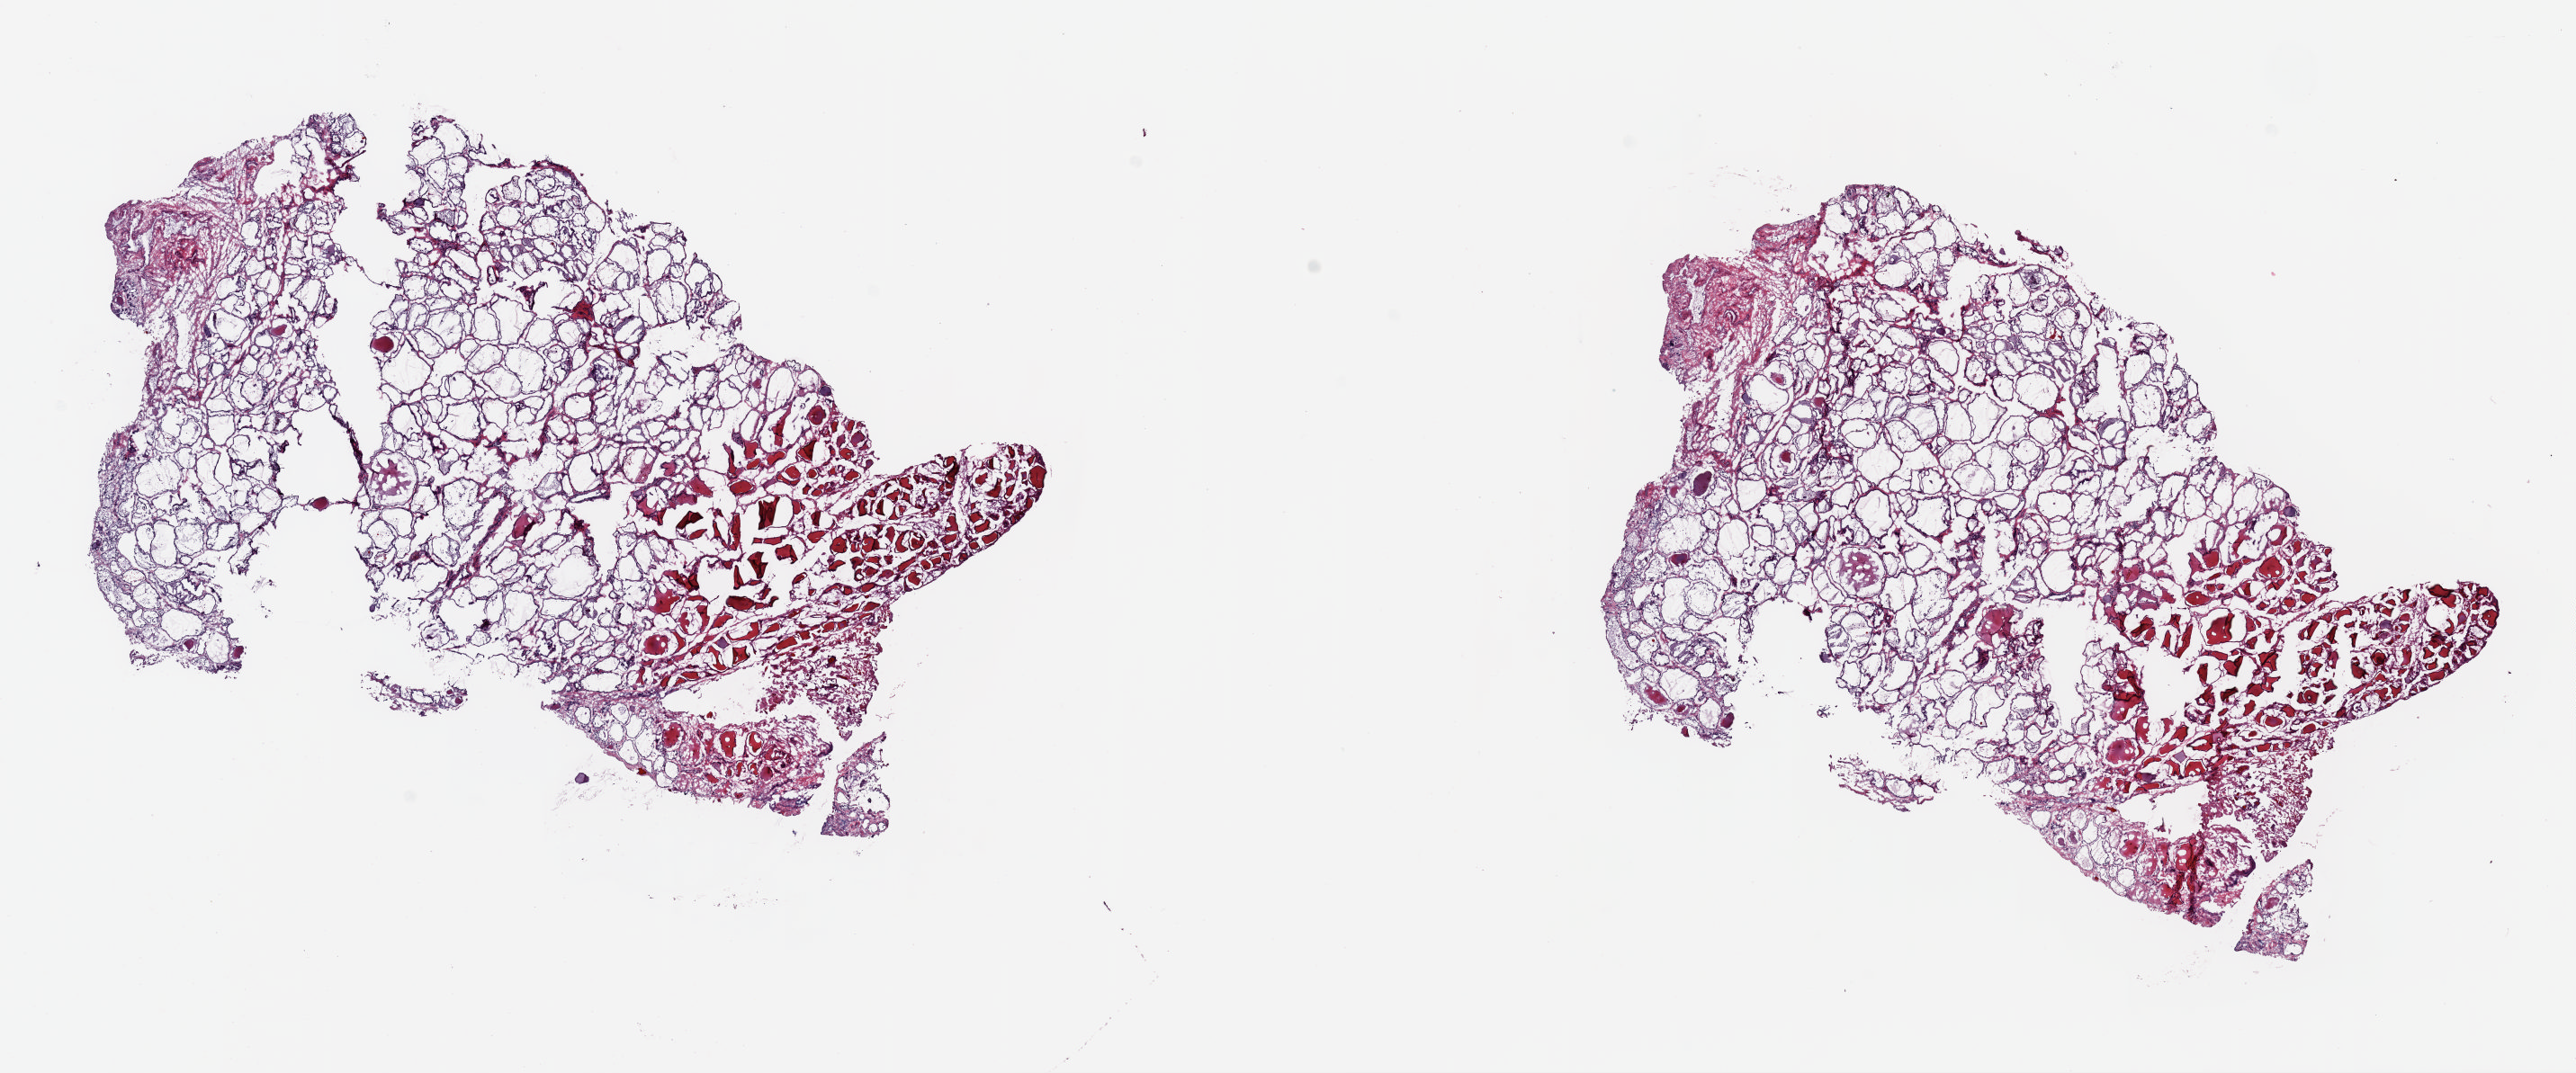
H&E whole-slide image, a low-resolution overview of the entire scanned area, about 22.6 x 9.4 mm (acquisition: 20x scan), frozen section, sample: solid tissue normal (non-tumour tissue), thyroid. Female, age 42 years at initial diagnosis. Composition of this section per pathologist review: tumour cells 0%, tumour nuclei 0%, normal cells 100%, stromal cells 0%, necrosis 0%. Inflammatory infiltration, as recorded: lymphocyte infiltration 0%, monocyte infiltration 2%, neutrophil infiltration 0%.
This section: solid tissue normal (non-tumour) sample from the same patient. Patient diagnosis: Papillary adenocarcinoma, NOS (thyroid gland).